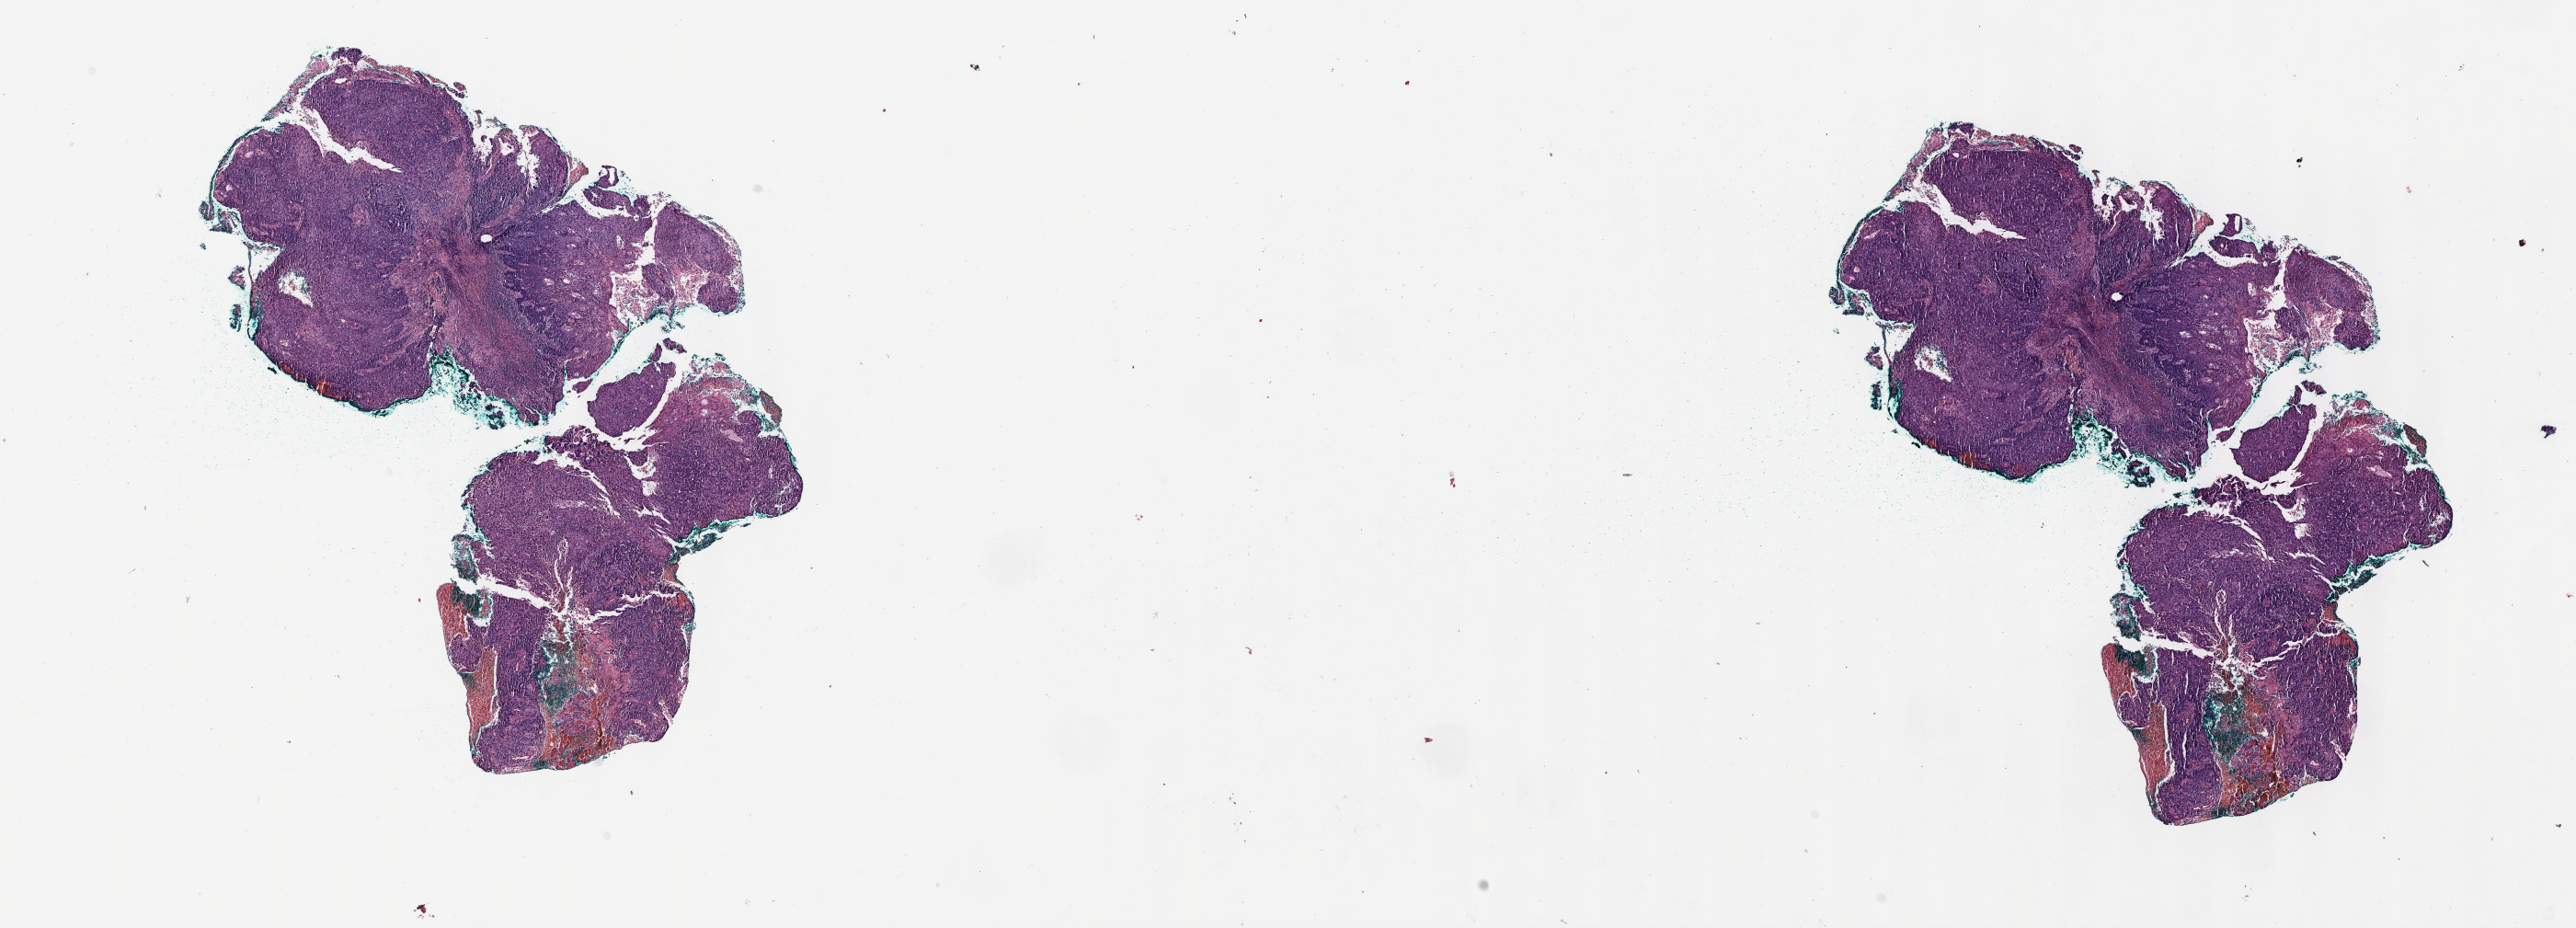
Digitized Hematoxylin and eosin (H&E) stained tissue section (whole slide) — shown as a low-resolution overview of the whole scanned area (about 22.7 x 8.2 mm). Formalin-fixed paraffin-embedded (FFPE) diagnostic section. Primary tumour sample from the cervix. Female, age 63 years at initial diagnosis. Histologic grade: GX (grade cannot be assessed).
- histologic diagnosis: Squamous cell carcinoma, NOS (cervix uteri)
- FIGO stage: IVA